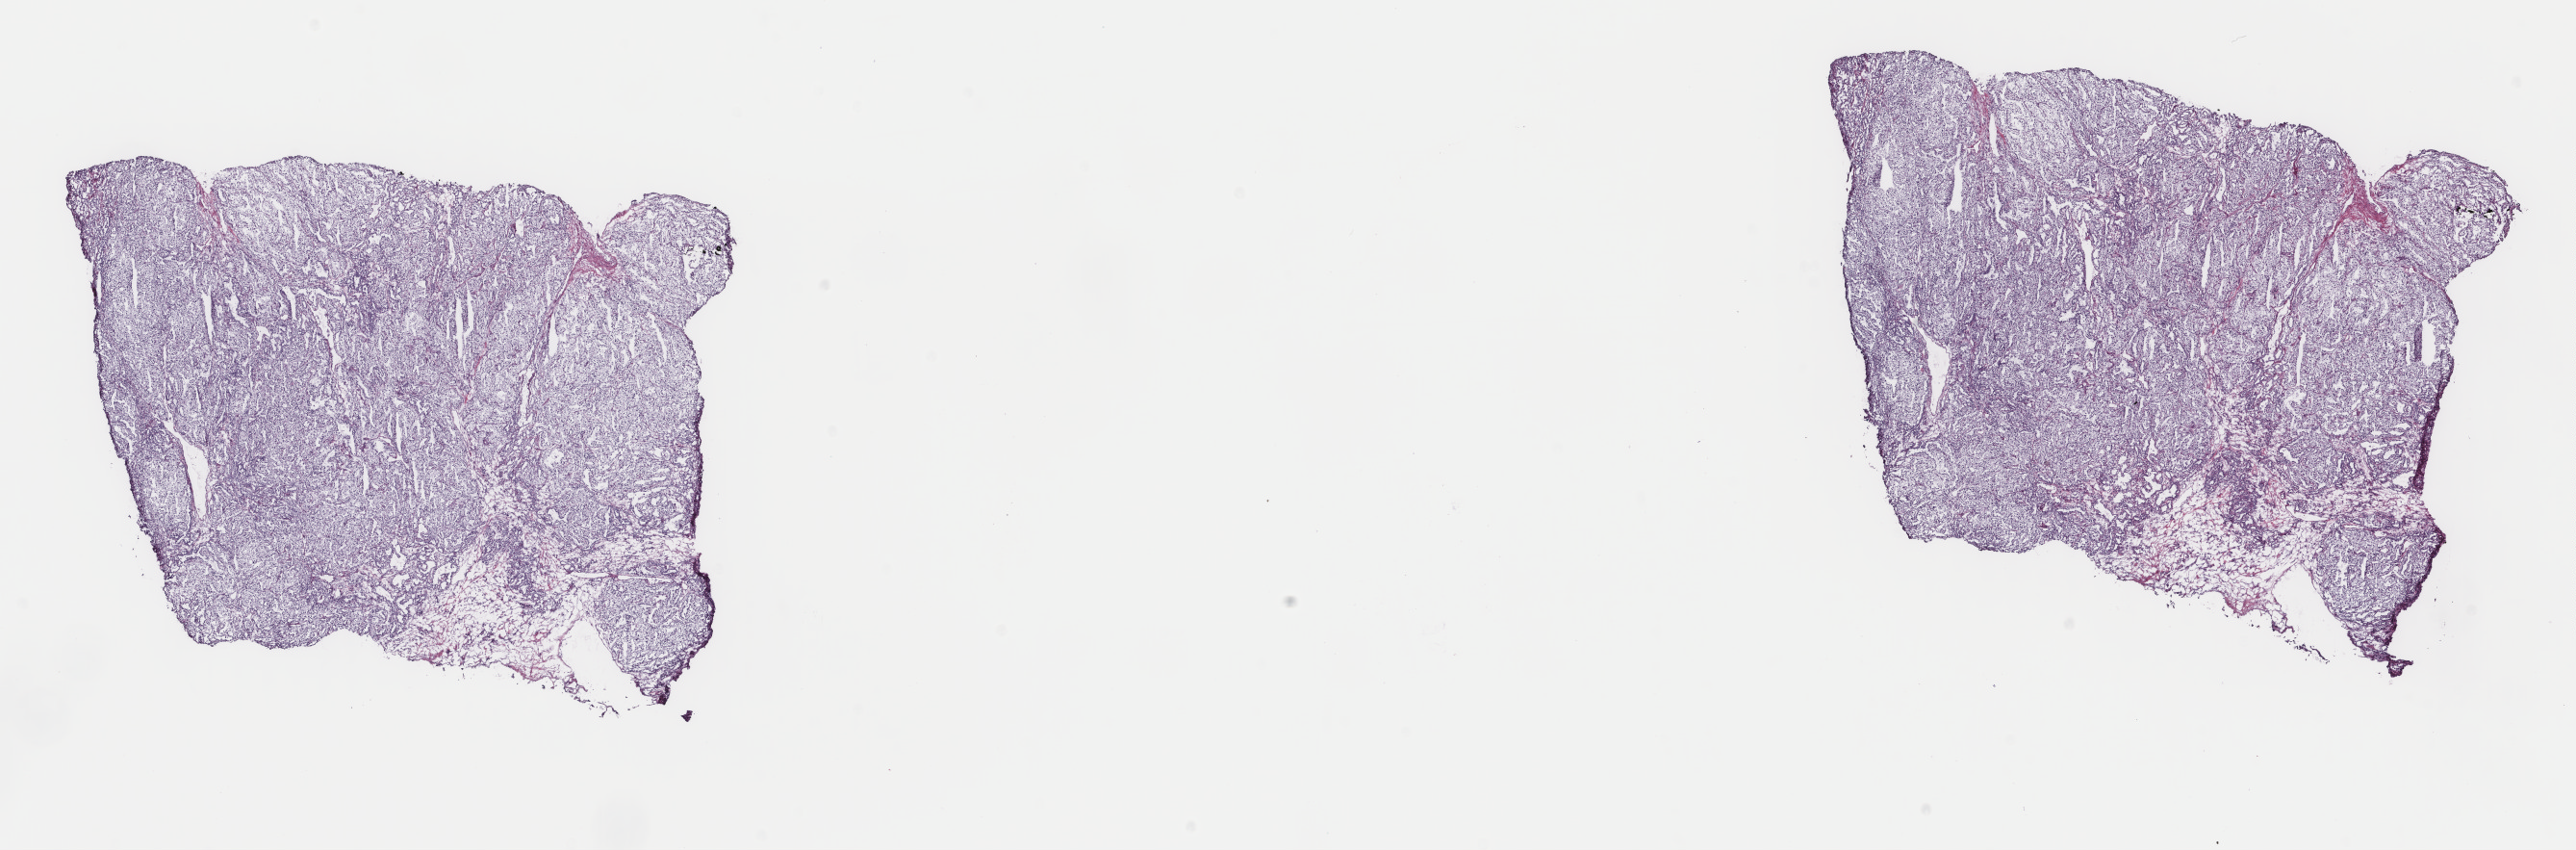
Hematoxylin and eosin (H&E) stained whole-slide image, a low-resolution overview of the entire scanned area, about 21.2 x 7.0 mm (slide scanned at 40x), frozen section from the top of the tissue portion, primary tumour sample from the kidney. Male, age 61 years at initial diagnosis. Histologic grade: G1 (well differentiated). Pathologist review of this section (percent, as recorded): tumour cells 100%, tumour nuclei 98%, normal cells 0%, stromal cells 0%, necrosis 0%. Inflammatory infiltration, as recorded: lymphocyte infiltration 0%, monocyte infiltration 0%, neutrophil infiltration 0%.
- AJCC pathologic stage: I (7th edition)
- histologic diagnosis: Renal cell carcinoma, NOS
- laterality: right